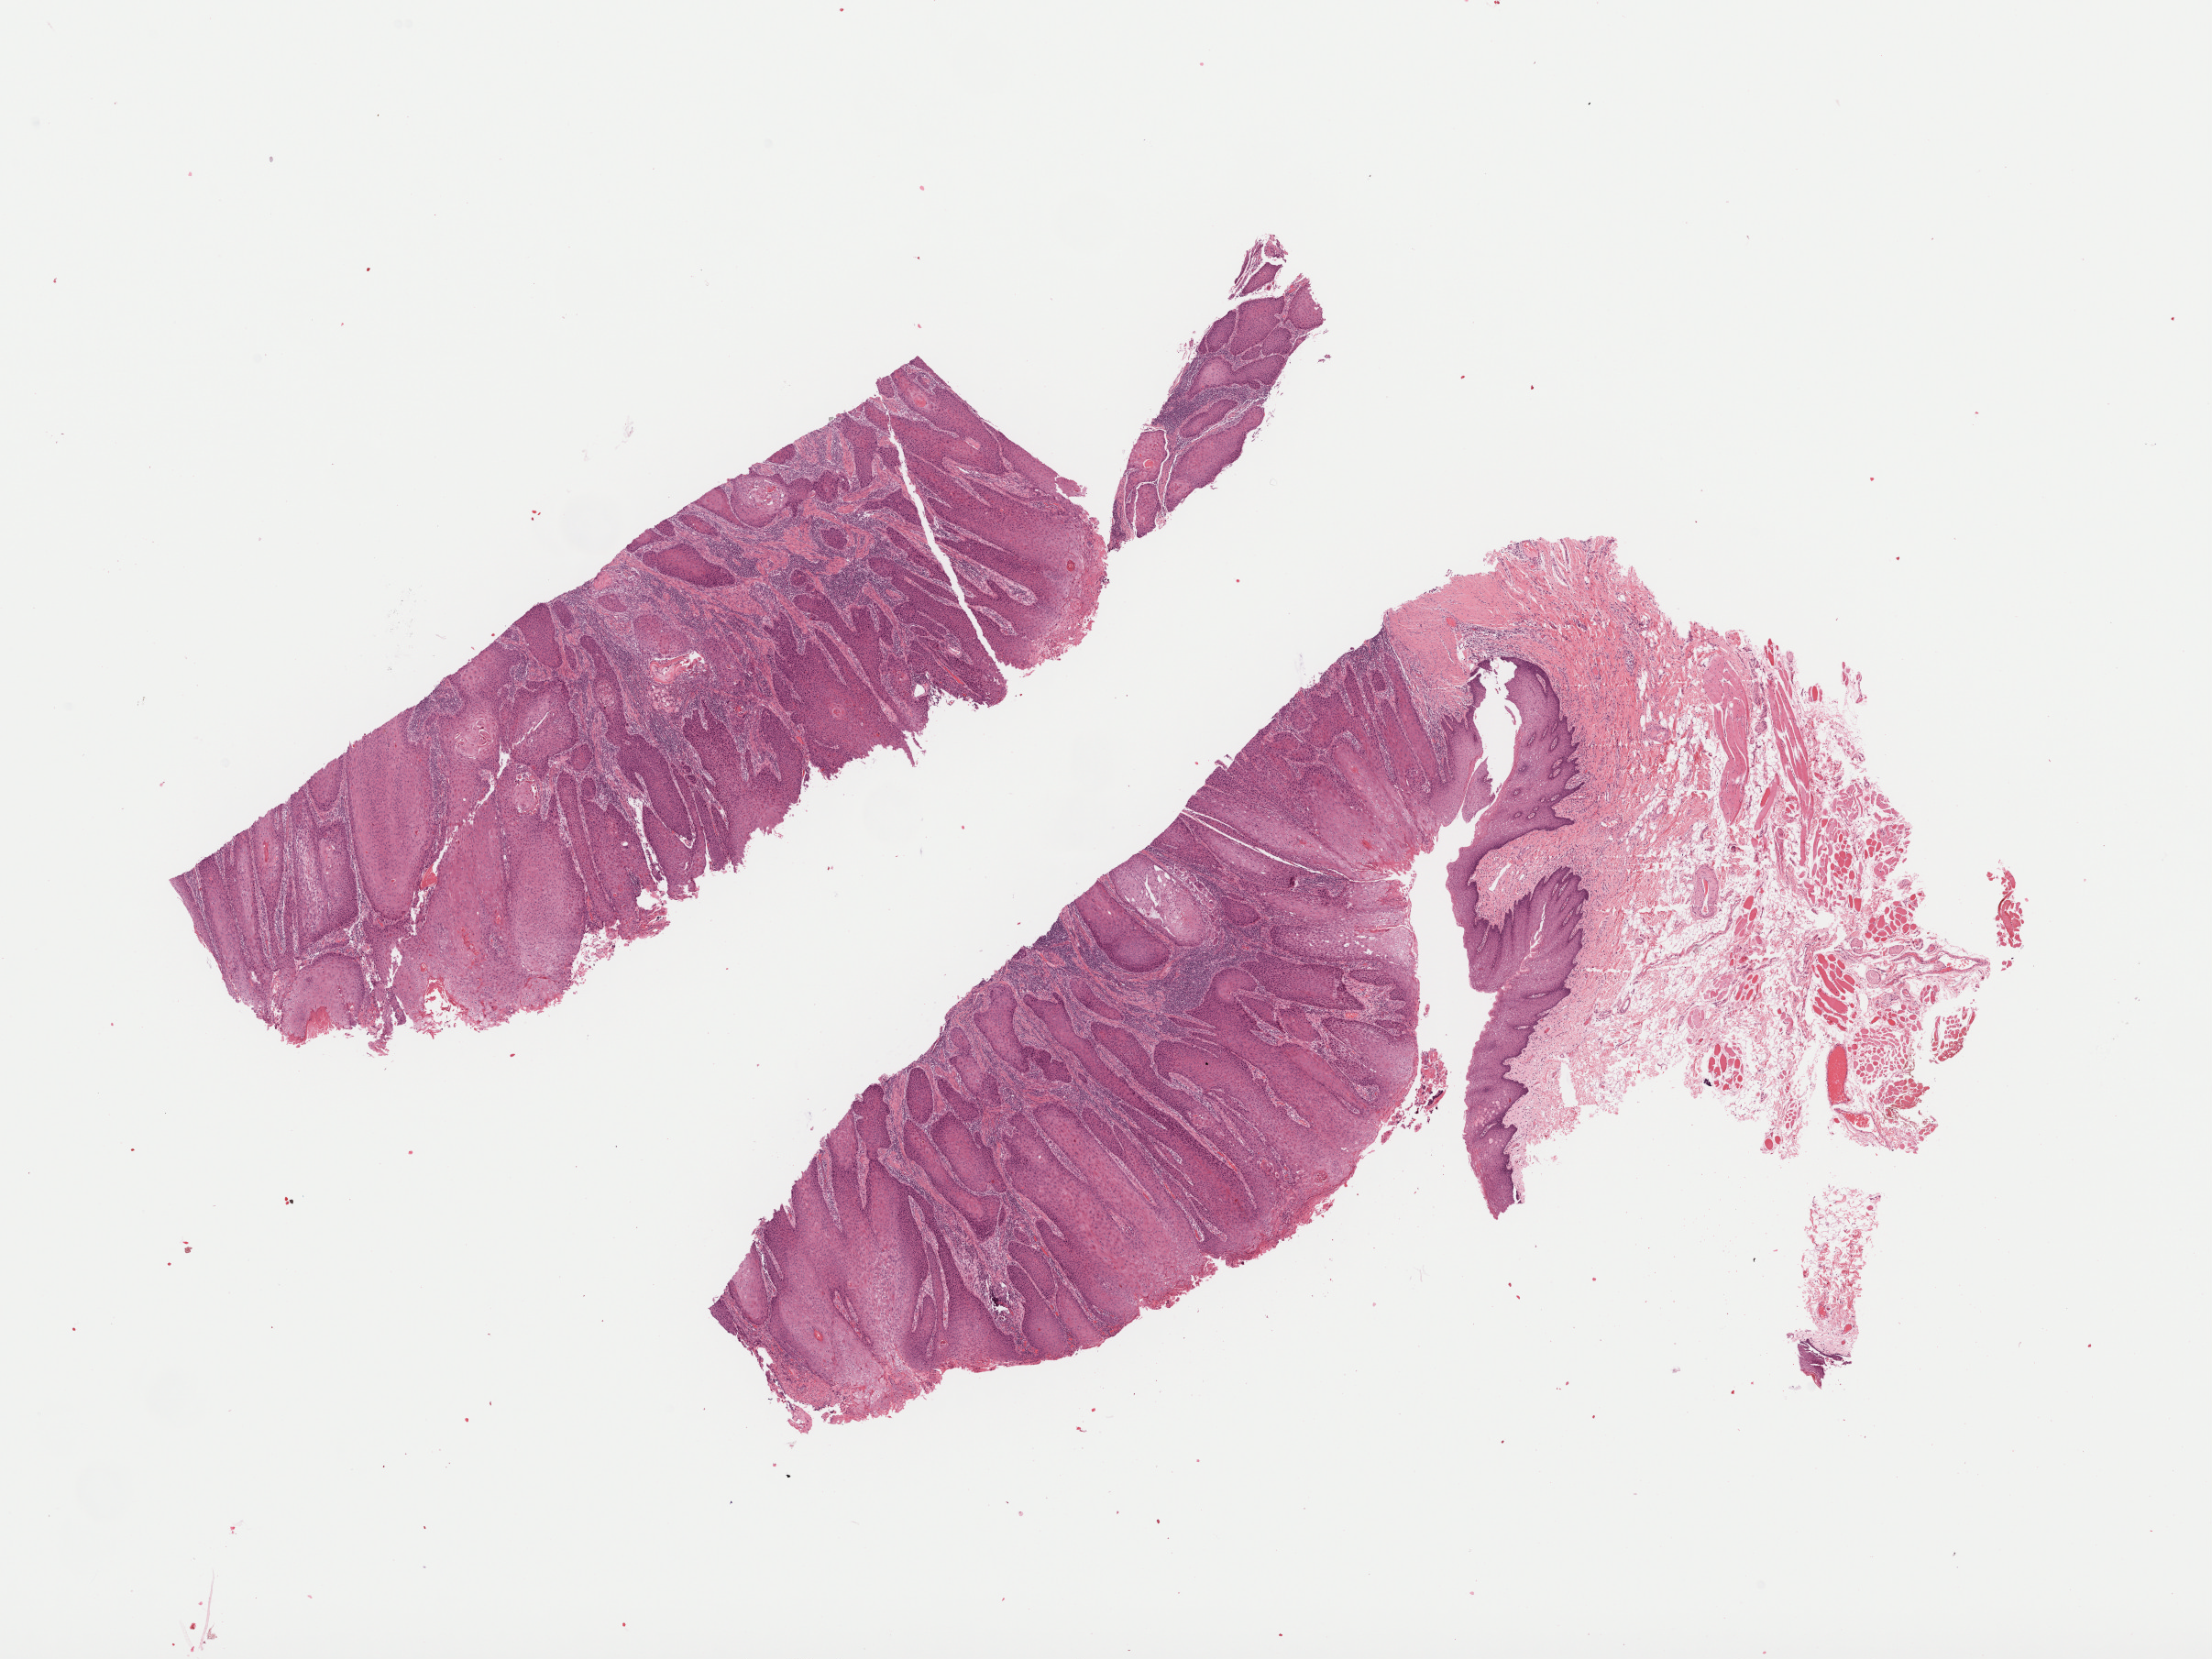
Whole-slide histology image, Hematoxylin and eosin (H&E) stained — a low-resolution overview of the entire scanned area, about 19.4 x 14.6 mm (slide scanned at 40x), formalin-fixed paraffin-embedded (FFPE) diagnostic section, sample: primary tumour, head and neck. Patient: male, age at initial diagnosis 69 years. Histologic grade: G2 (moderately differentiated).
Lymph nodes positive (case pathology): 0 of 32 examined. Pathologic diagnosis: Squamous cell carcinoma, NOS. AJCC pathologic stage: II.